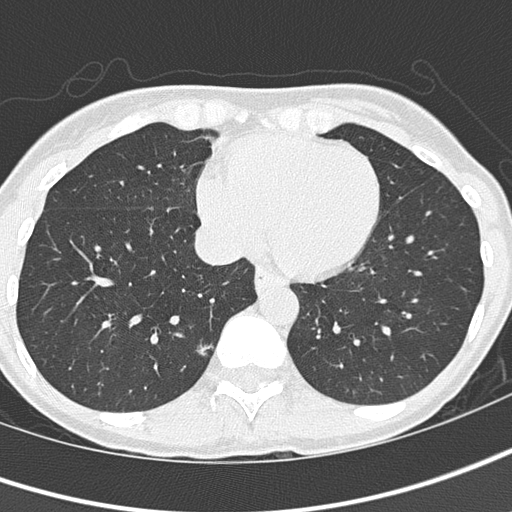
Low-dose screening chest CT, one axial slice. Reconstruction kernel B50f. 120 kVp. Lung window (W 1500 / L -600 HU). 2 mm slice thickness. 512 × 512 image matrix, field of view 276 × 276 mm.
Outlined on this slice (manually delineated by an expert):
- lesion 1 (tumor, lower lobe of right lung): bounding box (x1, y1, x2, y2) in pixels: (197, 345, 213, 355)